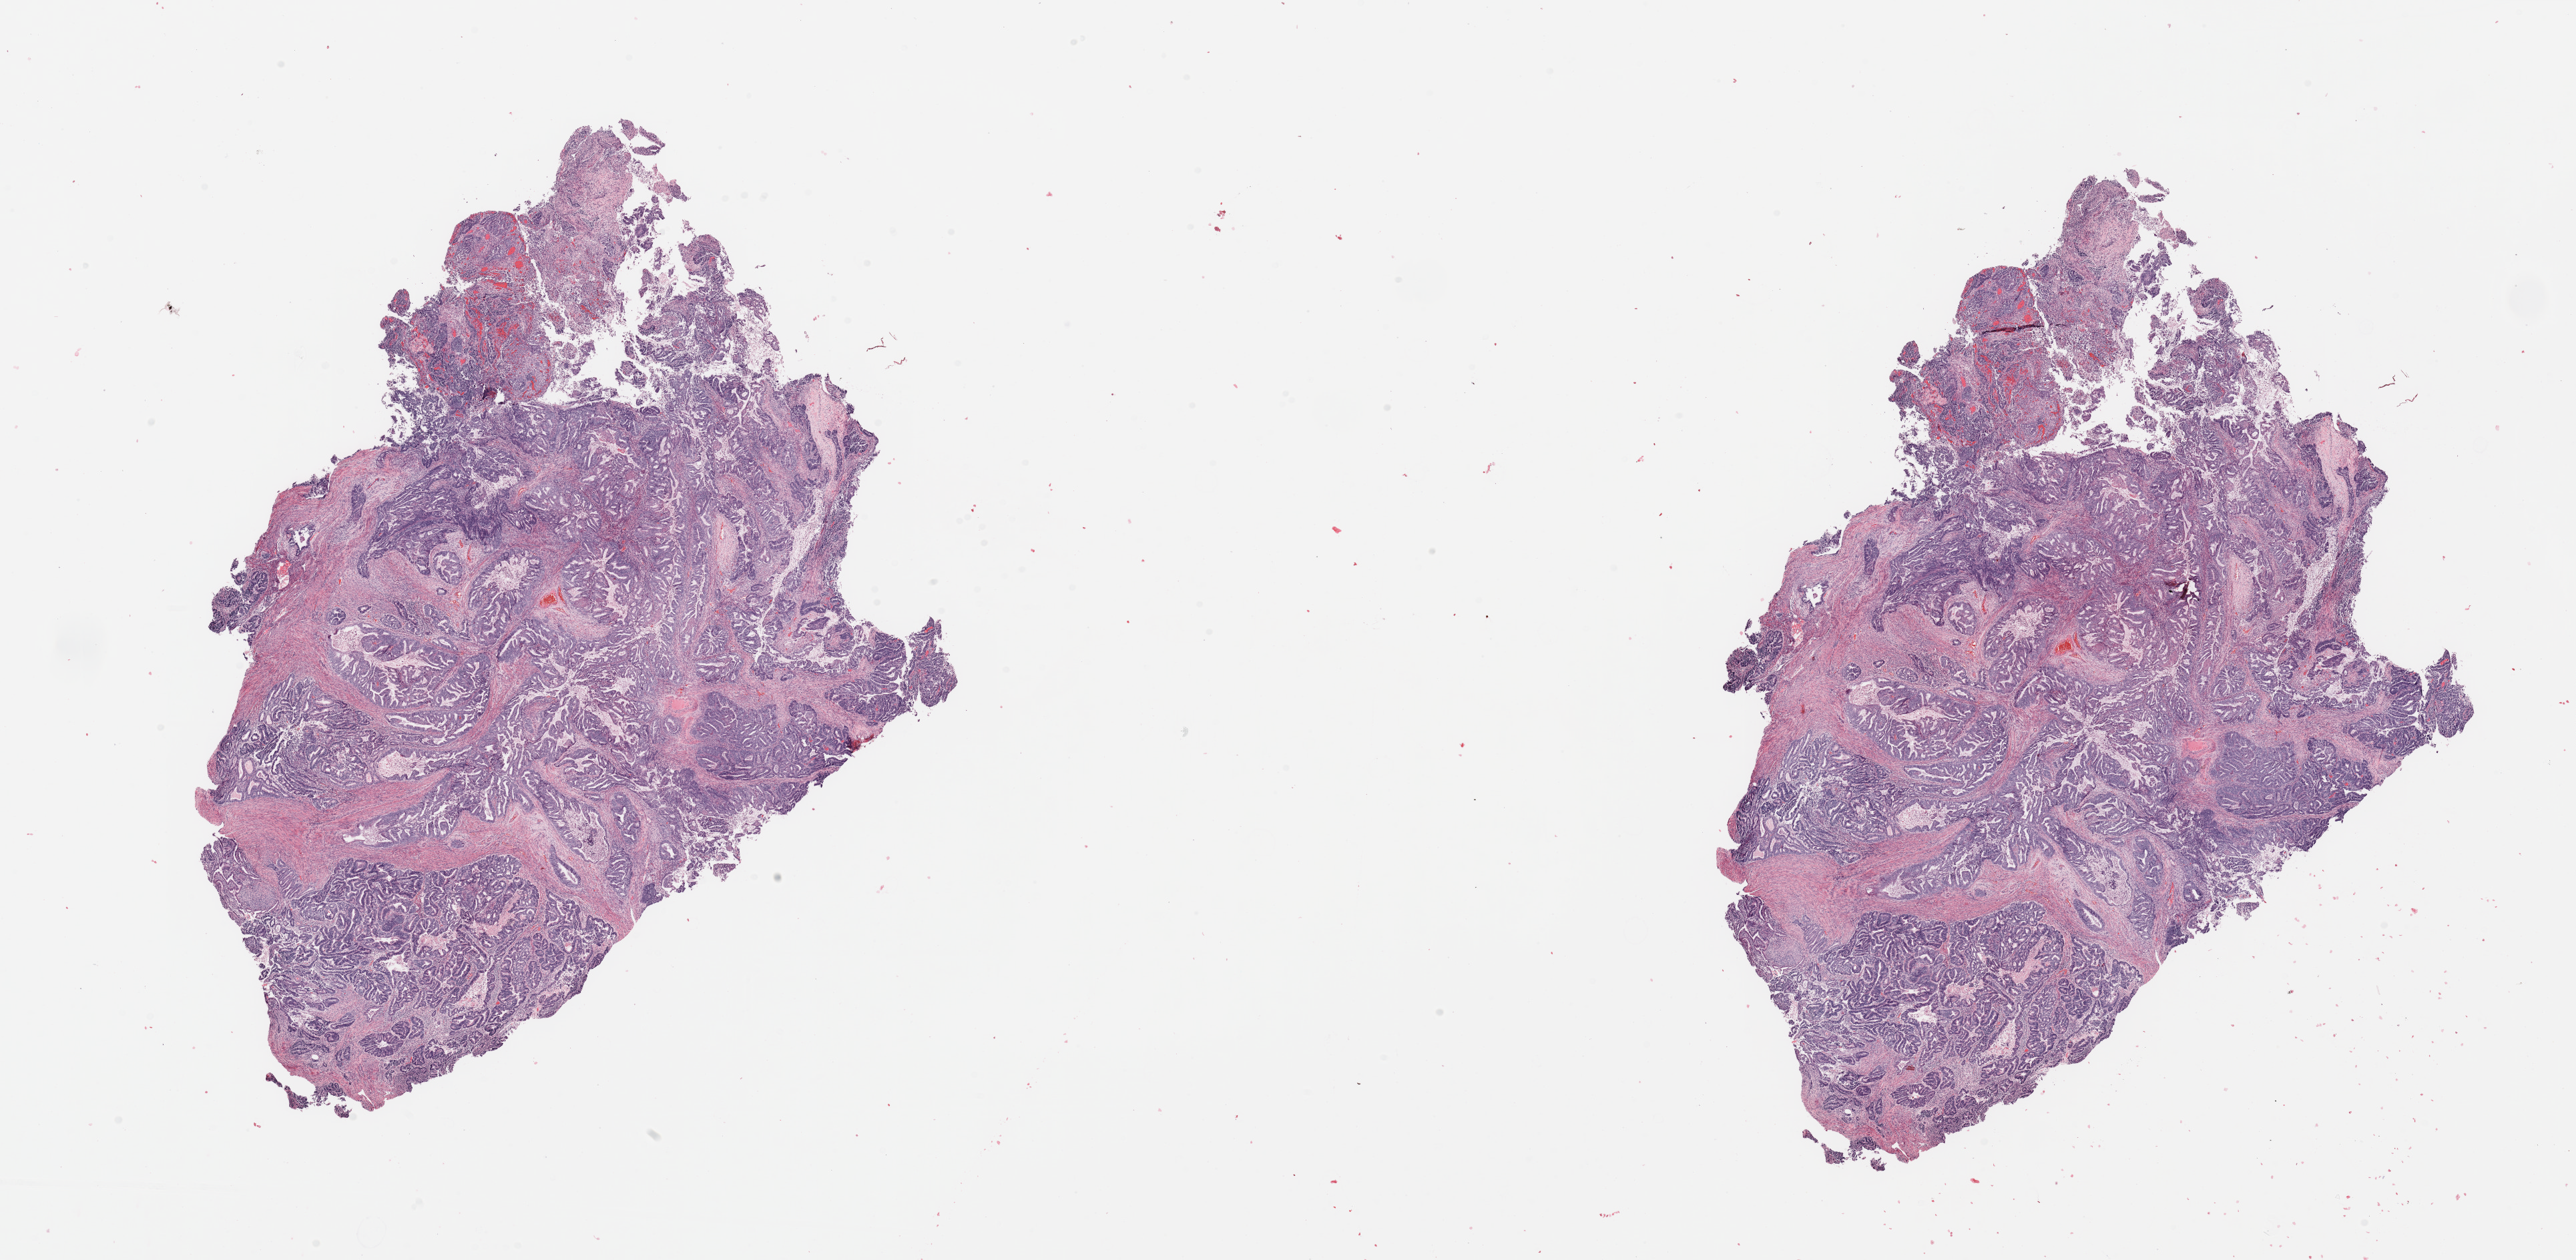
Digitized H&E-stained tissue section (whole slide) — shown as a low-resolution overview of the whole scanned area (about 30.5 x 14.9 mm, from a 20x scan); tumour tissue sample, uterus. Patient: female, age 53 years. Histologic grade: G2 (moderately differentiated).
AJCC pathologic stage: I. Histologic diagnosis: Endometrioid adenocarcinoma, NOS.